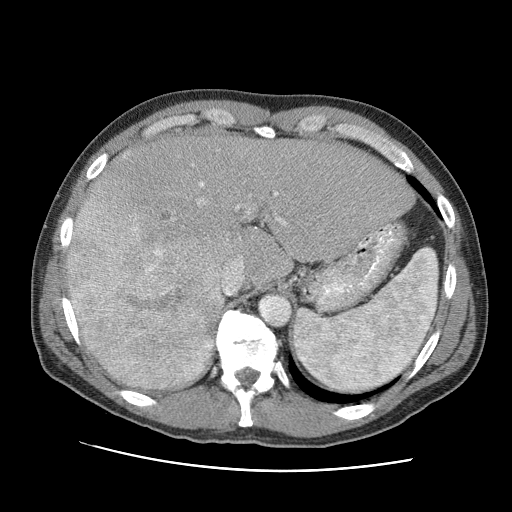
Contrast-enhanced abdominal CT (liver protocol), one axial slice; position 68 of 95 along the scan axis; reconstruction kernel STANDARD; one of 2 acquisitions stored at this slice position; soft-tissue window (W 400 / L 40 HU); 2.5 mm slice thickness; 512 × 512 image matrix, field of view 360 × 360 mm. From the clinical record (not read from this slice): diagnosis: hepatocellular carcinoma (patient treated with transarterial chemoembolisation; whether this scan precedes or follows treatment is not stated here); TNM stage (as recorded): Stage-IVA; Child-Pugh class: A; tumour differentiation: moderately differentiated.
Annotated regions visible in this slice (semi-automatic segmentation, software-assisted and operator-edited):
- liver parenchyma outside the tumour (the mass and vessels are separate outlines, so this box may not span the whole liver): bounding box (x1, y1, x2, y2) in pixels: (66, 134, 414, 388)
- mass: (65, 149, 222, 390)
- liver vessels: (159, 164, 287, 296)